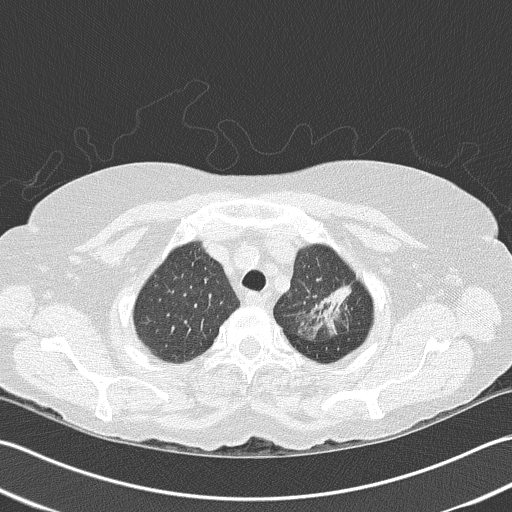
Low-dose screening chest CT, axial slice, first (baseline) screen, lung window (W 1500 / L -600 HU), 2 mm slice thickness, 120 kVp, slice 134 of 159 in the series, 512 × 512 image matrix. Female participant, aged 68 years at enrolment. Former smoker at enrolment.
Expert reader's lesion annotation, bounding box (x1, y1, x2, y2) in pixels: (291, 262, 364, 333). Screening reader's record for this exam: no non-calcified nodule ≥4 mm recorded.